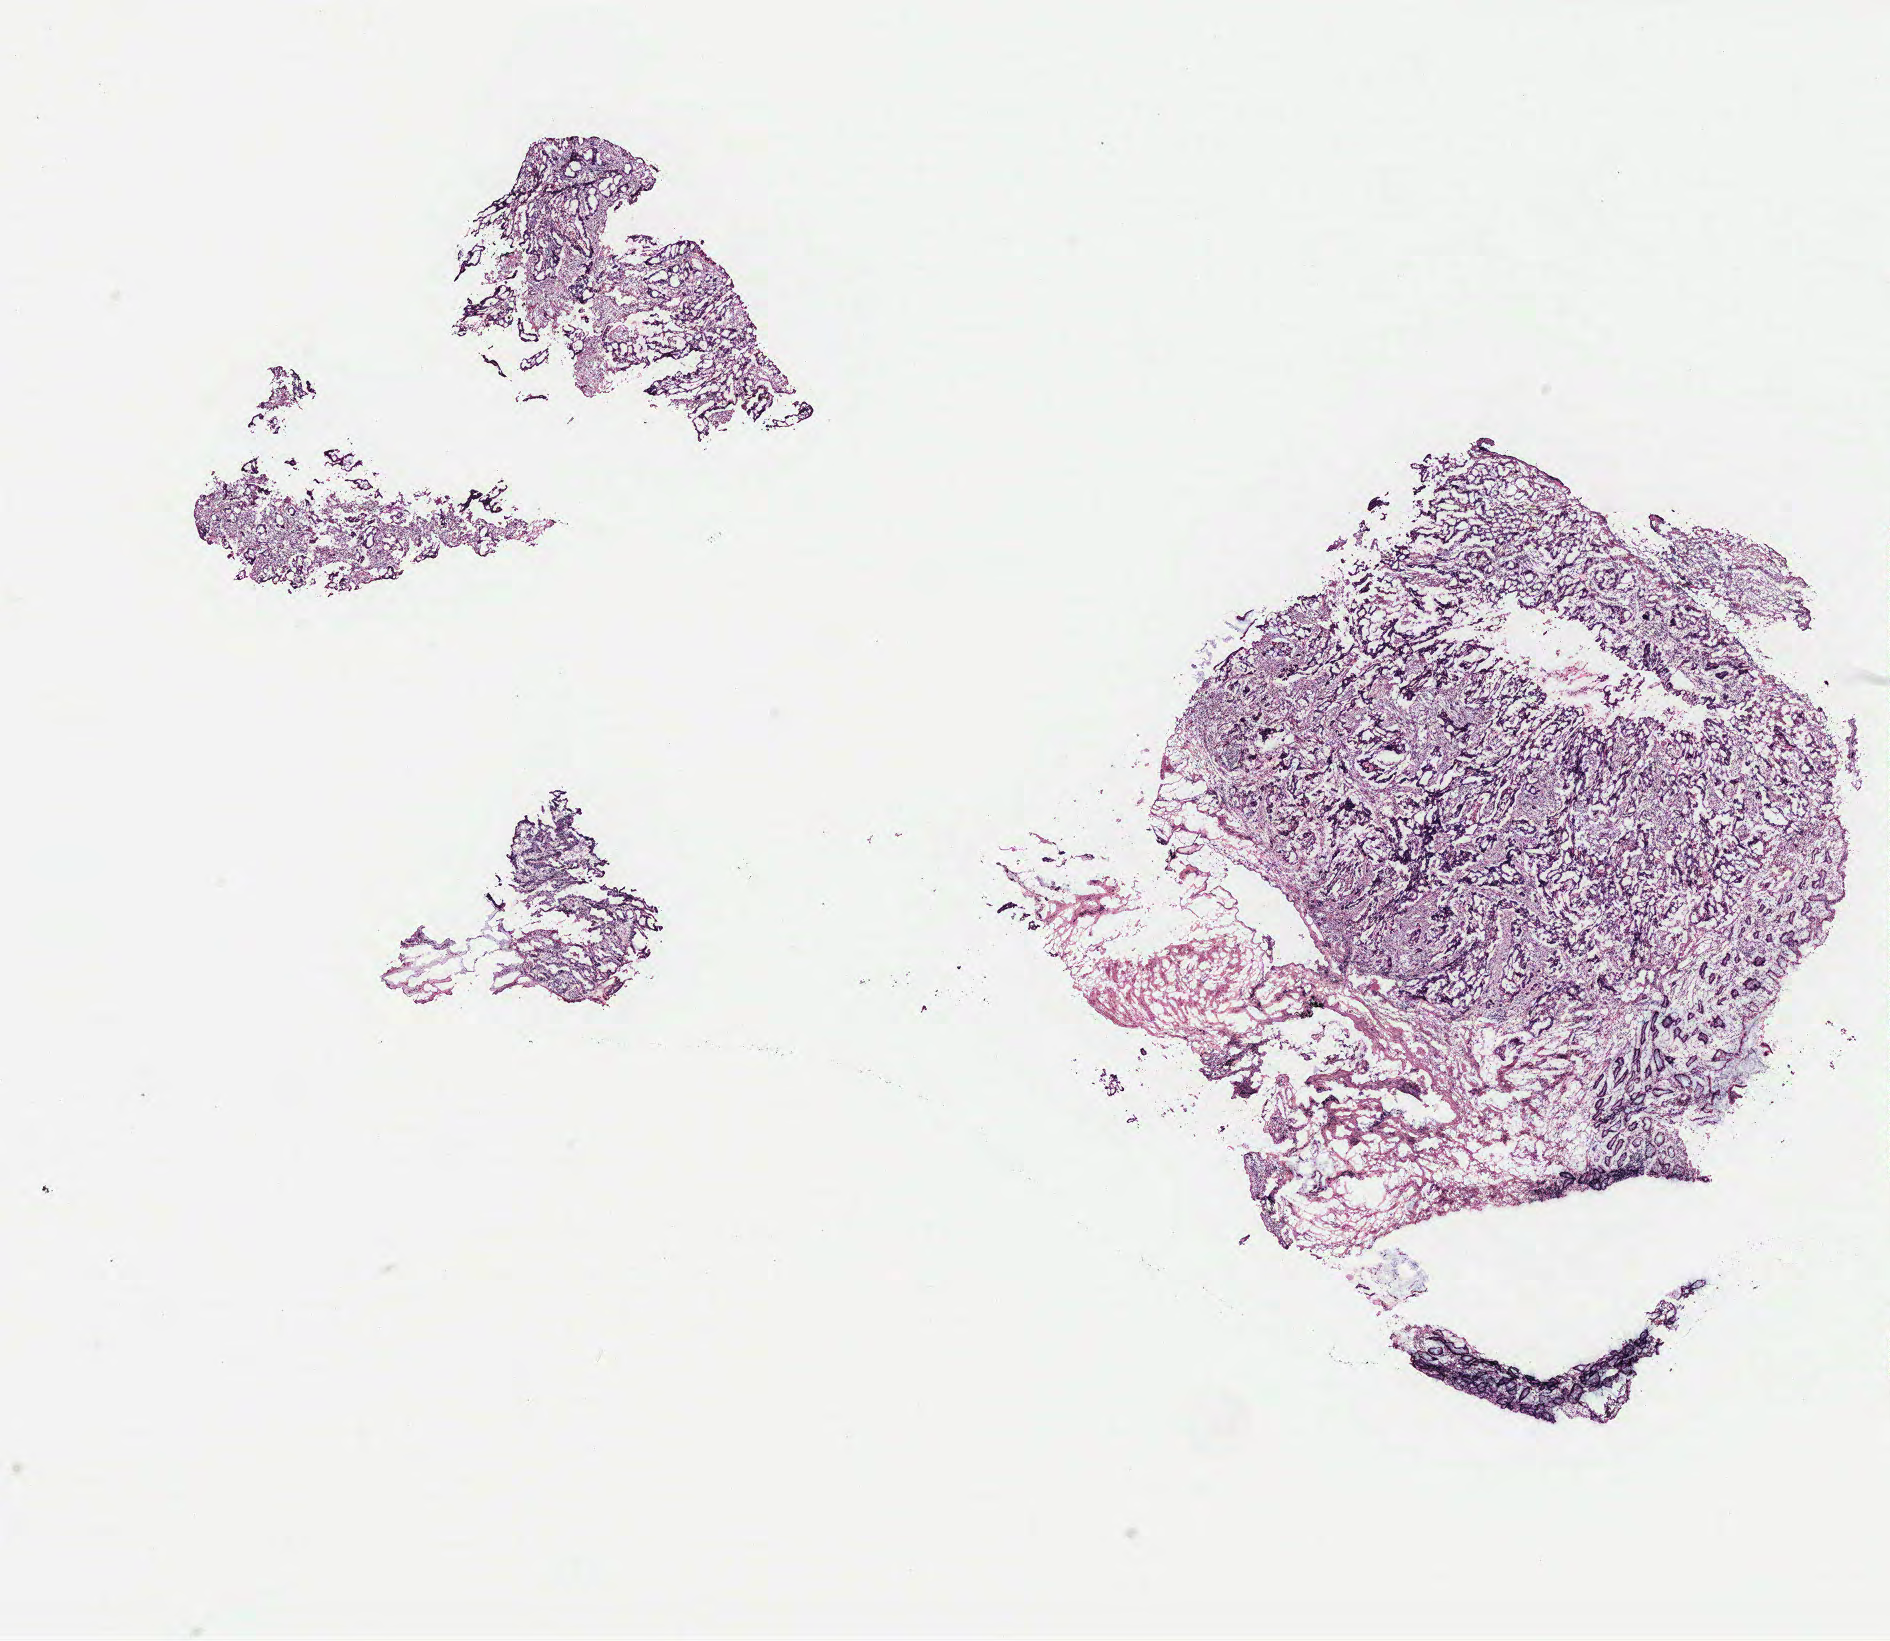
Whole-slide histology image, Hematoxylin and eosin (H&E) stained, shown as a low-resolution overview of the whole scanned area (about 15.1 x 13.1 mm); colon, tissue type not recorded.
• patient diagnosis (cohort enrolment): colon cancer (colon)